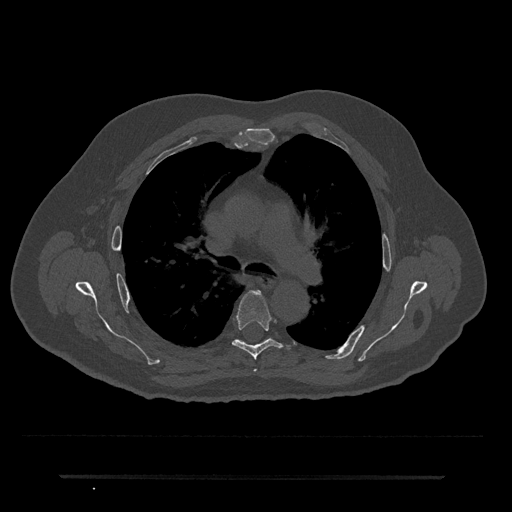
CT including the spine, one axial slice; slice 482 of 797 in the series (ordered by position); reconstruction kernel Br40s/3; 120 kVp; bone window (W 1800 / L 400 HU); 0.5 mm slice thickness; 512 × 512 image matrix, field of view 437 × 437 mm. Male patient, age 69 years. Case-level facts recorded for this patient, not image findings: primary cancer: prostate.
Structures marked on this image (semi-automatically segmented with operator editing):
- T5 vertebra: box from (x=232, y=290) to (x=291, y=359) px